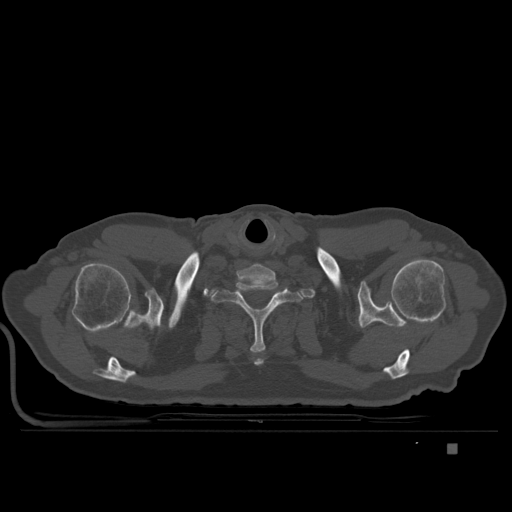
CT including the spine, one axial slice. Slice 326 of 435 in the series (ordered by position). Bone window (W 1800 / L 400 HU). 1.5 mm slice thickness. 512 × 512 image matrix. Patient: male, 73 years. Case-level facts recorded for this patient, not image findings: primary cancer: skin.
Outlined on this slice (semi-automatic segmentation, software-assisted and operator-edited):
- T1 vertebra: box from (x=210, y=280) to (x=303, y=353) px